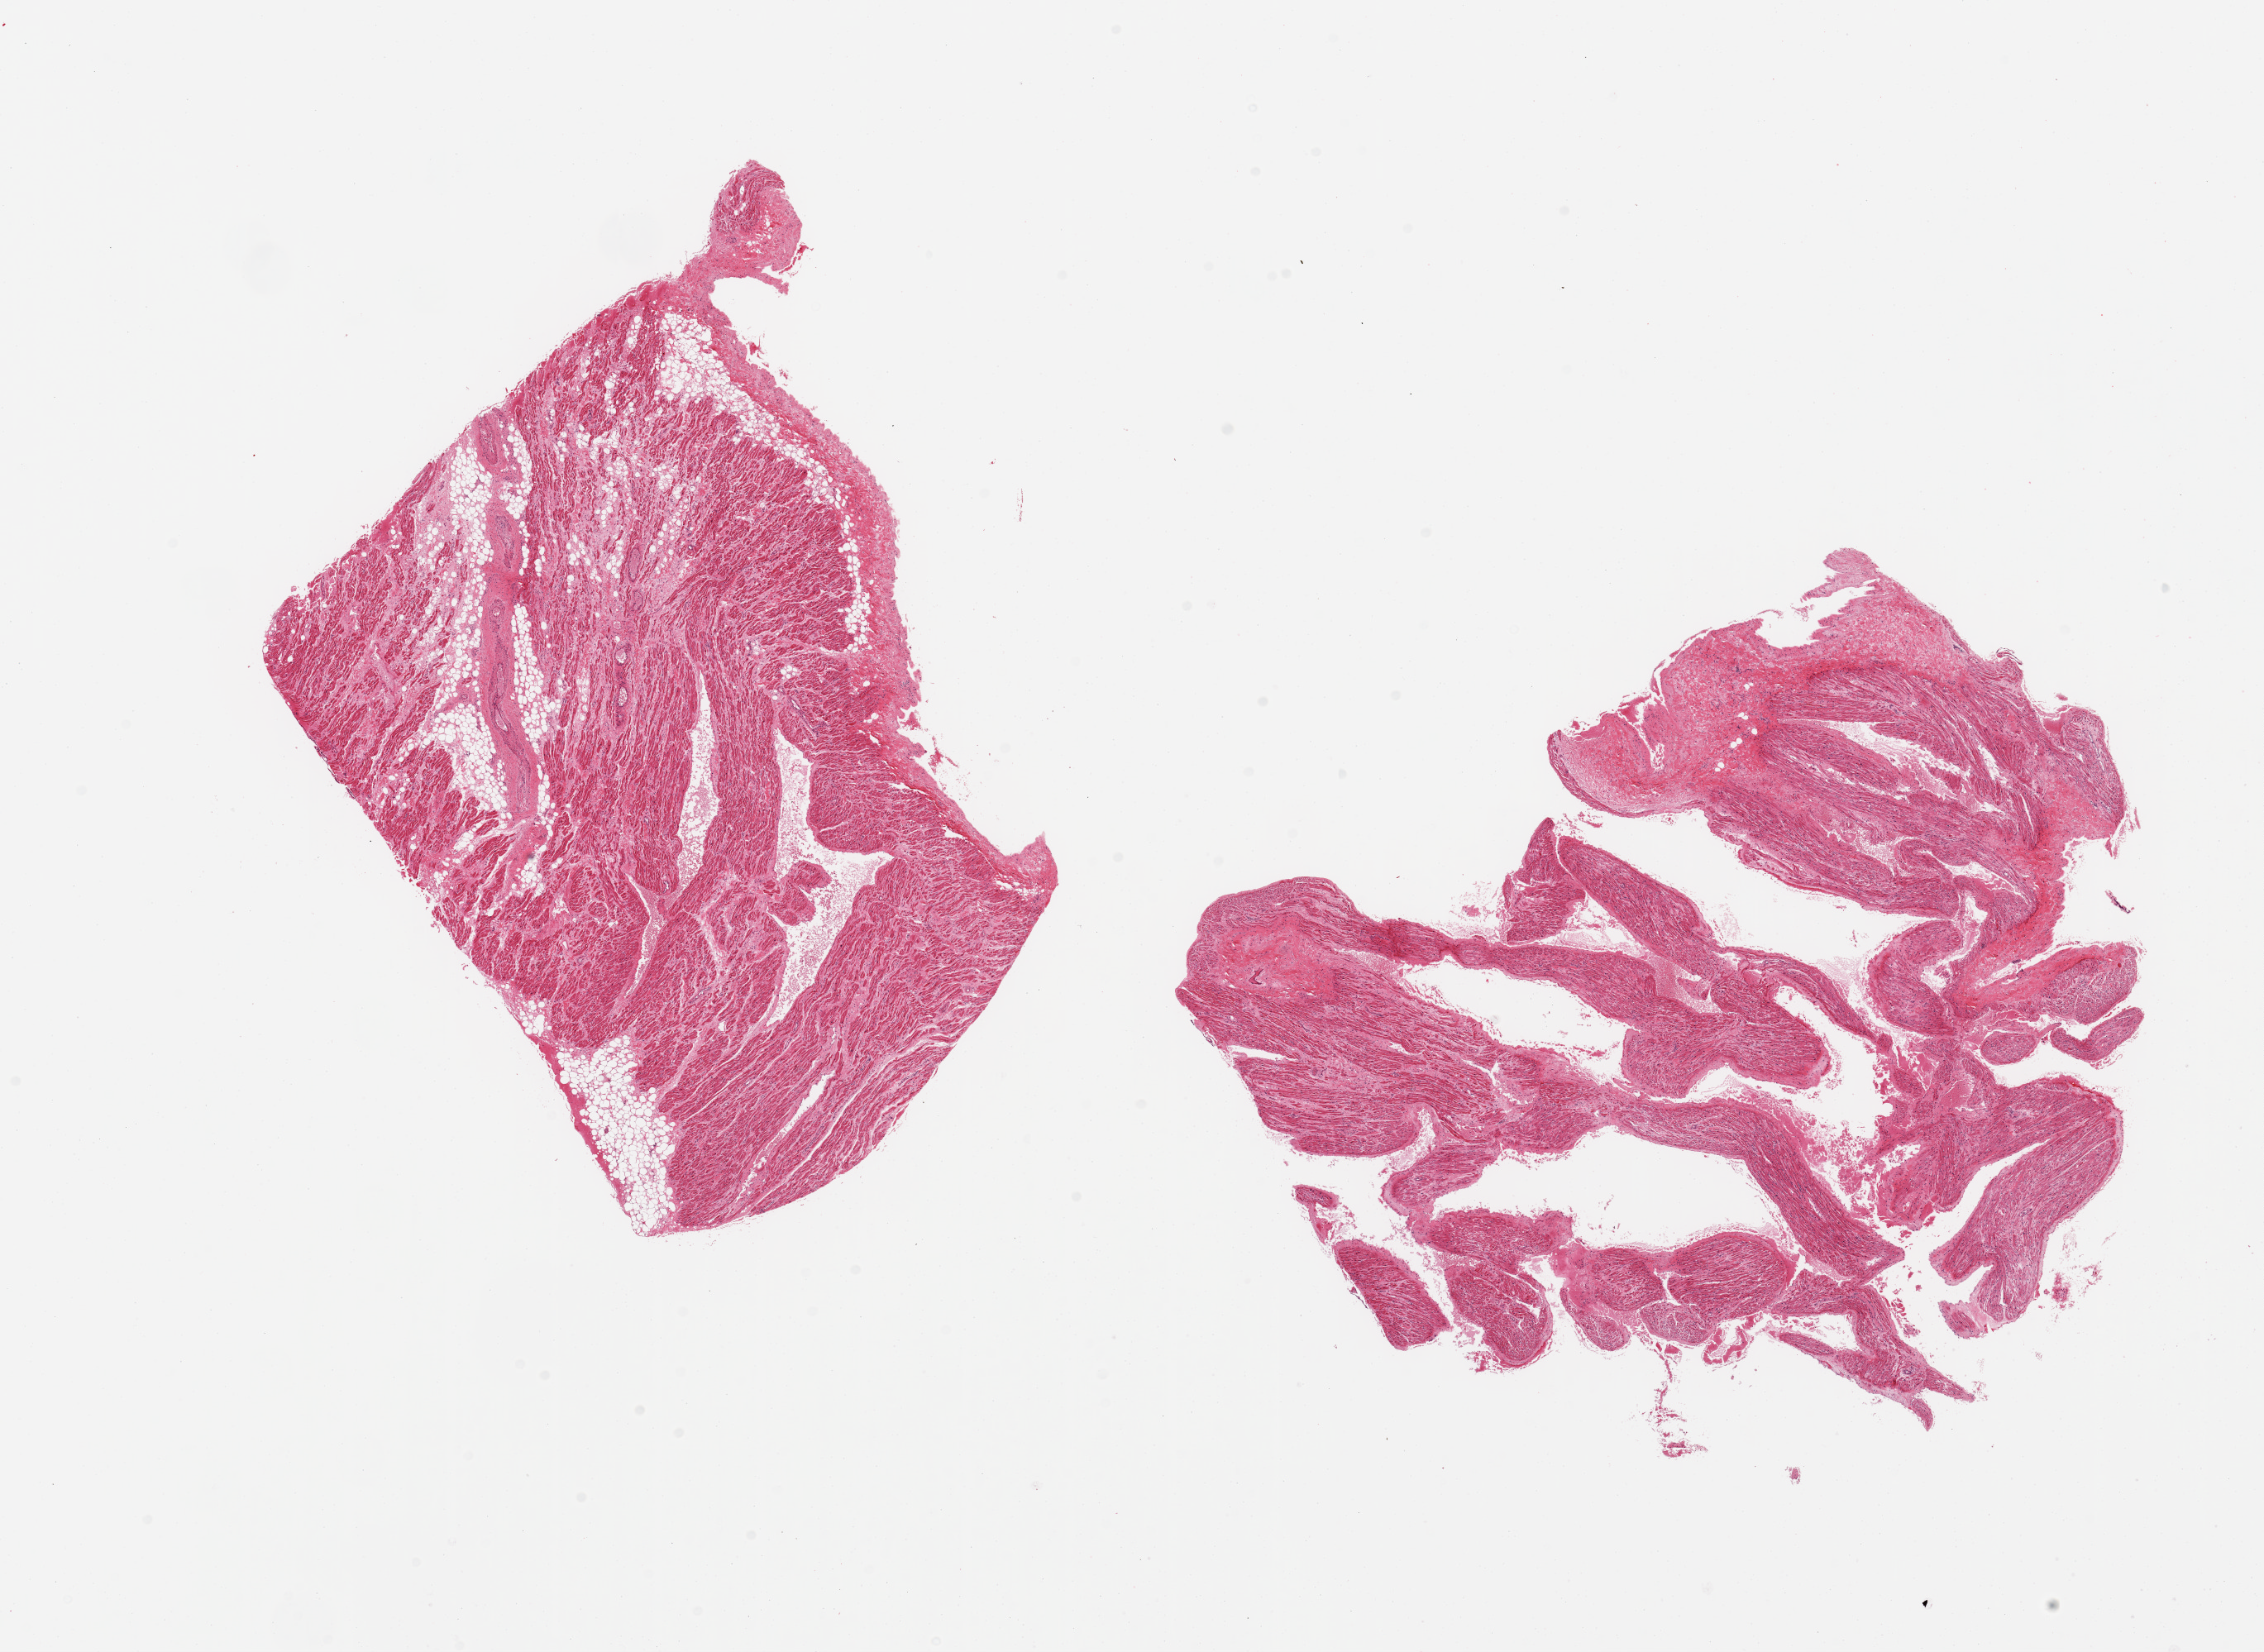
Haematoxylin and eosin whole-slide image — low-resolution overview of the scanned area, about 21.7 x 15.8 mm. PAXgene-fixed paraffin-embedded (PFPE) section. Section of auricular appendage (target tissue). Tissue donor sample.
Pathologist's review note for this sample: 2 pieces; 10% internal fat.